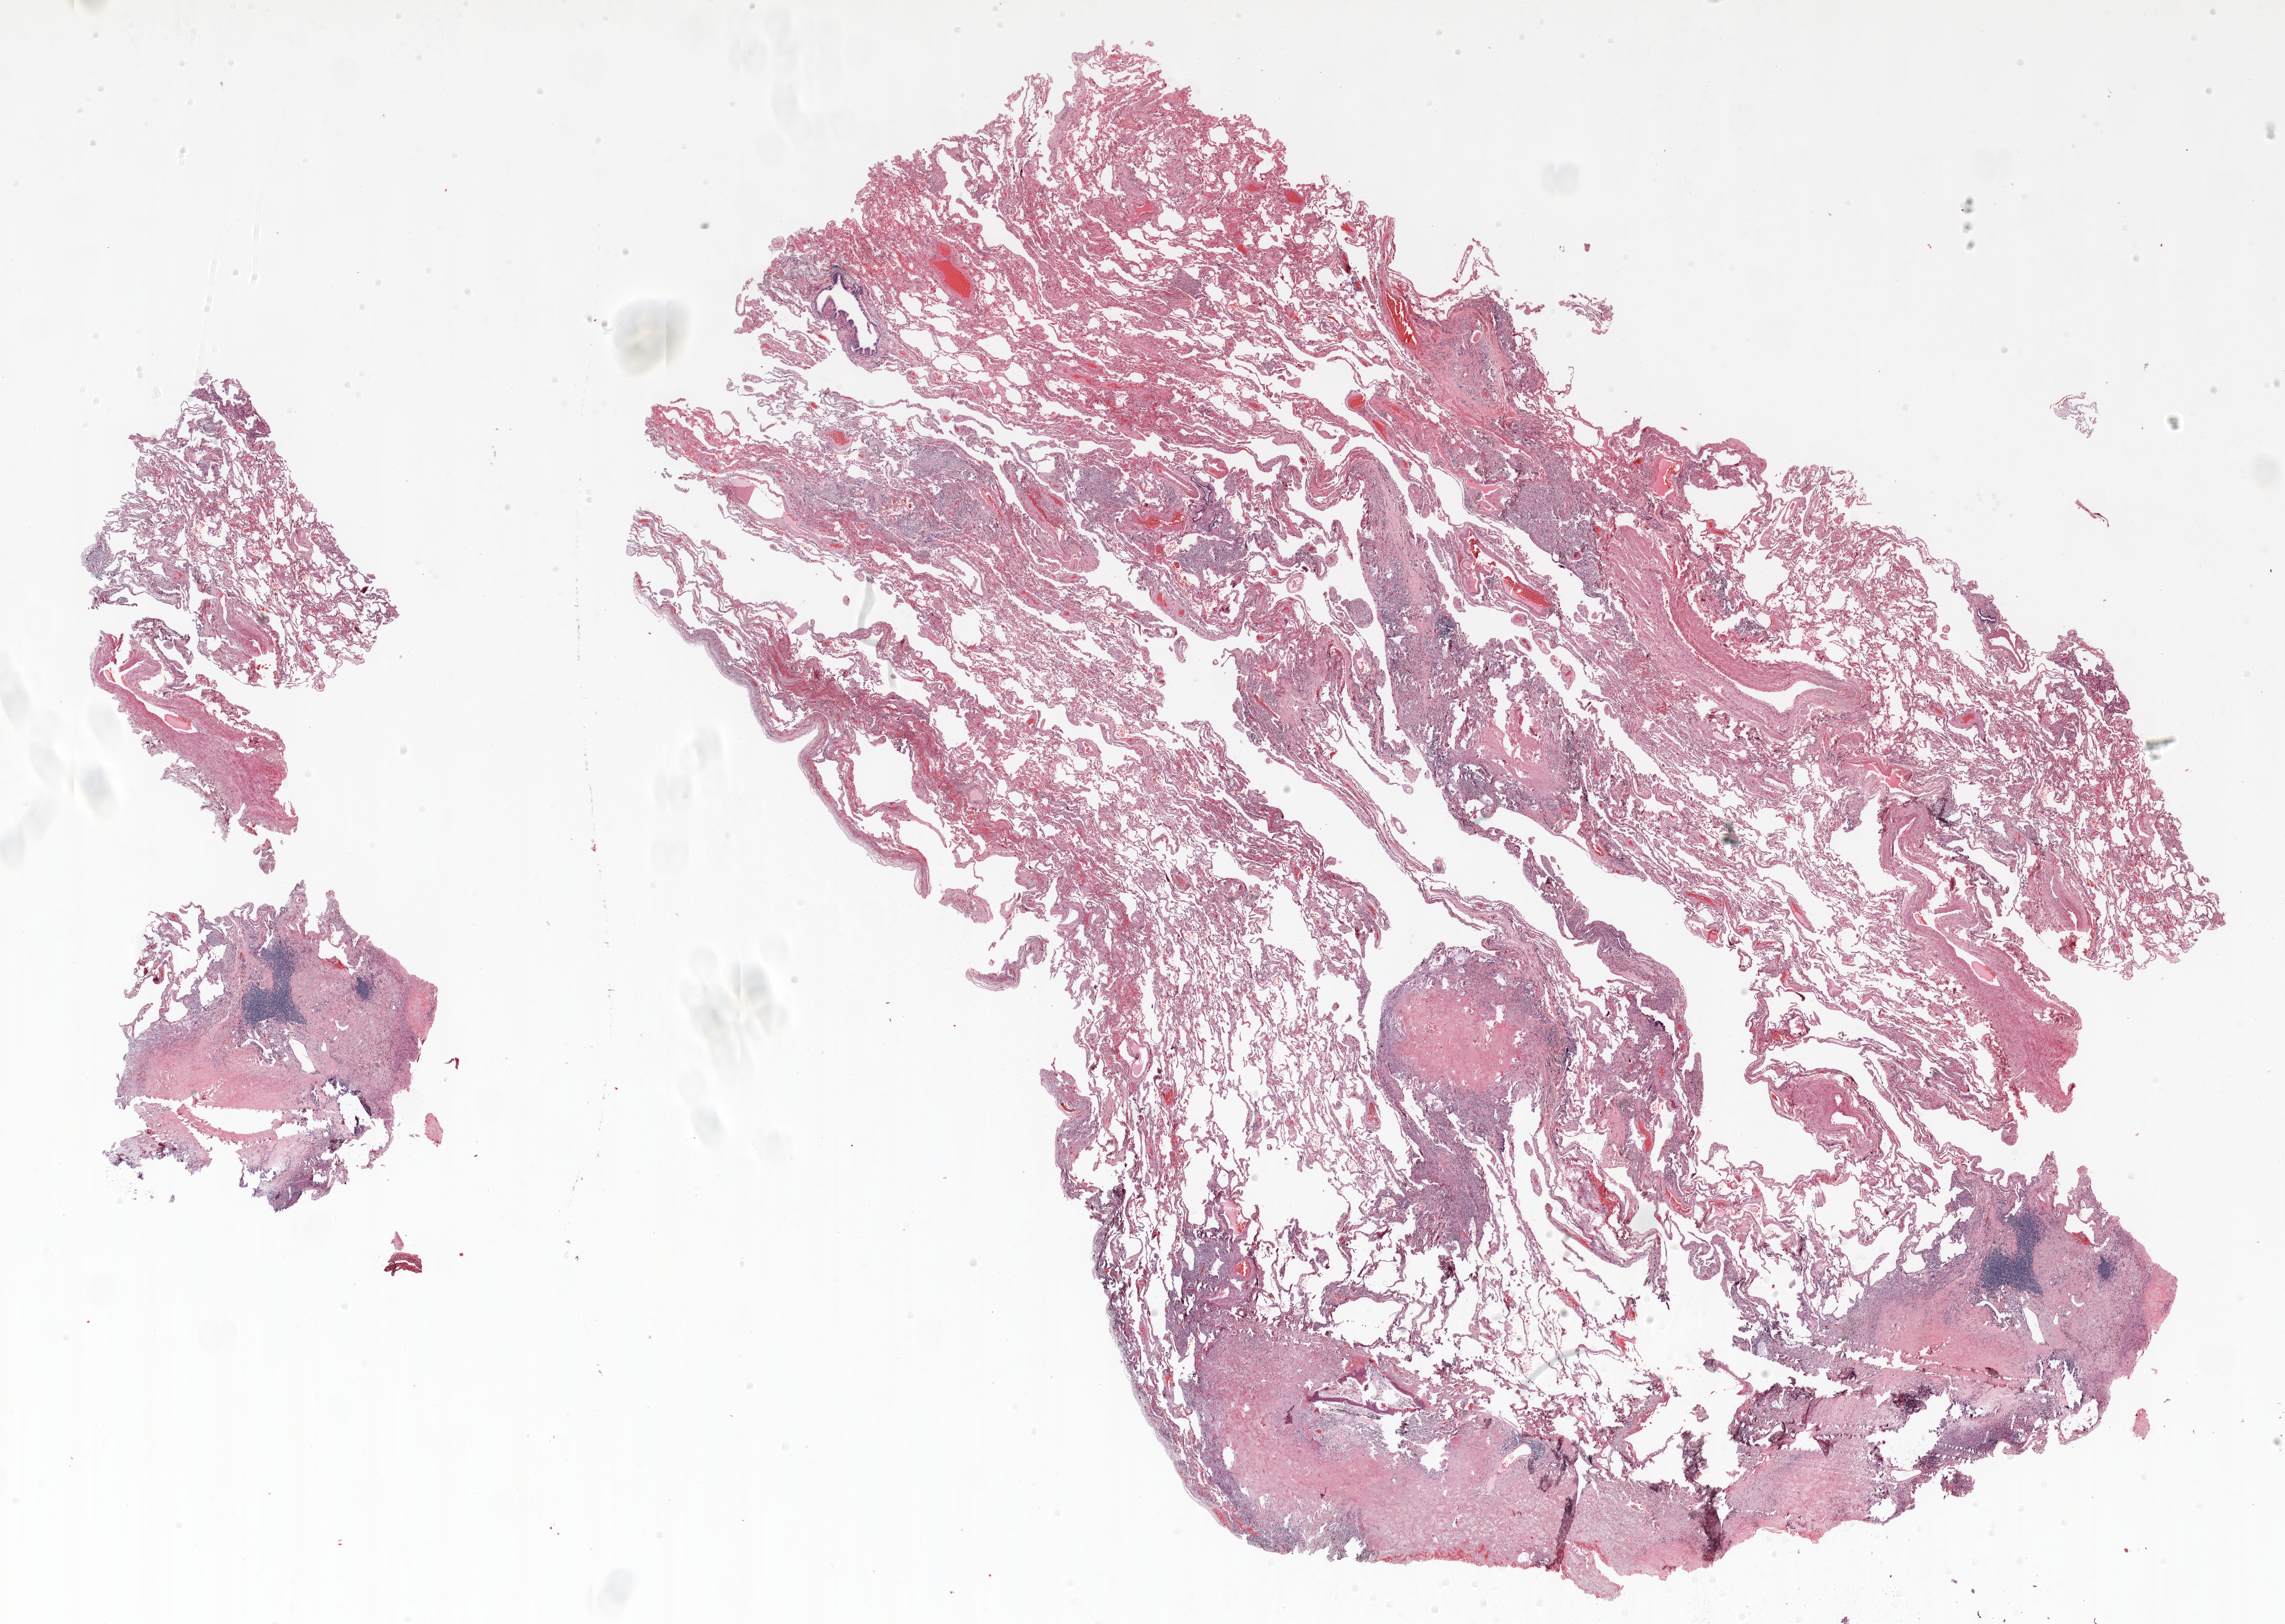
H&E-stained whole-slide image, low-resolution overview of the scanned area, about 31.0 x 22.1 mm (acquisition: 20x scan). FFPE section. Lung tissue. Male patient, aged 65 at enrolment. Former smoker at enrolment.
Participant's lung-cancer diagnosis: Adenocarcinoma, NOS (ICD-O-3 8140/3).